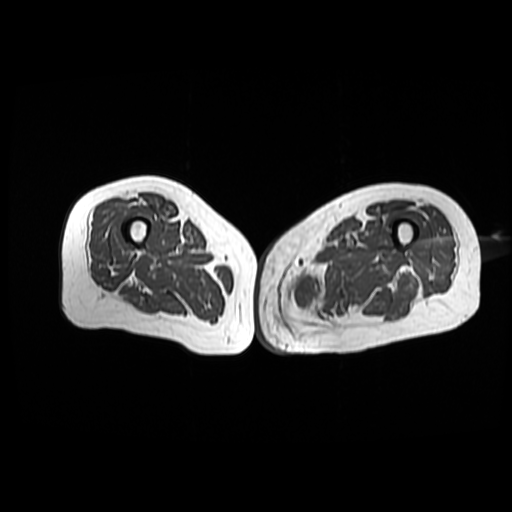
MRI of an extremity soft-tissue mass, one axial slice; slice 41 of 42 in the series (ordered by position); 6 mm slice thickness; 512 × 512 image matrix, field of view 420 × 420 mm. Female patient. Case-level facts recorded for this patient, not image findings: histological type: pleomorphic leiomyosarcoma; grade: high; site of the primary tumour: left thigh.
Annotated regions visible in this slice (outlined manually by an expert reader):
- gross tumour volume including surrounding oedema: box from (x=288, y=267) to (x=354, y=307) px